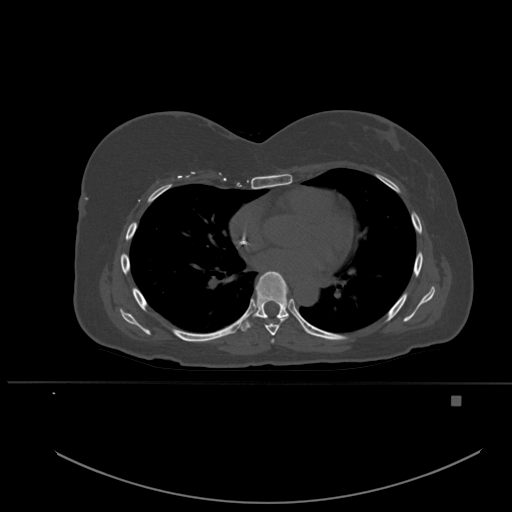
CT including the spine, one axial slice. Slice 342 of 651 in the series (ordered by position). Bone window (W 1800 / L 400 HU). 1.5 mm slice thickness. 512 × 512 image matrix. Female patient, age 49 years. Case-level facts recorded for this patient, not image findings: primary cancer: breast; vertebrae with lytic lesions (as recorded): L3, T12, L4.
Outlined on this slice (semi-automatic segmentation, software-assisted and operator-edited):
- T5 vertebra: bounding box [x1, y1, x2, y2] px = [271, 339, 274, 343]
- T6 vertebra: [265, 317, 288, 336]
- T7 vertebra: [240, 271, 301, 331]